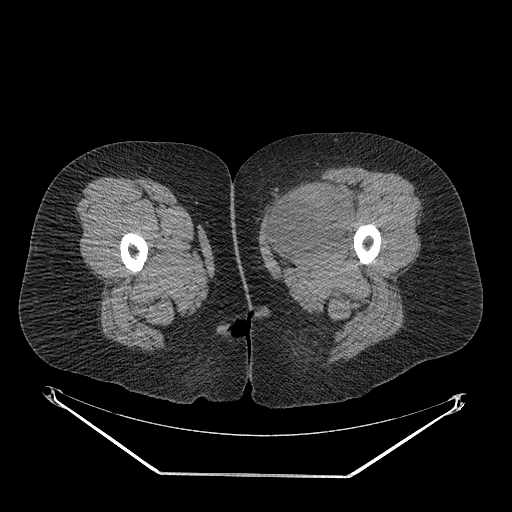
CT of an extremity soft-tissue mass (from a PET/CT study), one axial slice. Slice 26 of 267 in the series (ordered by position). Reconstruction kernel STANDARD. Soft-tissue window (W 400 / L 40 HU). 3.75 mm slice thickness. 512 × 512 image matrix, field of view 500 × 500 mm. Female patient. Case-level facts recorded for this patient, not image findings: histological type: myxofibrosarcoma; grade: intermediate; site of the primary tumour: left thigh.
Annotated regions visible in this slice (expert contour drawn on MRI and transferred to this co-registered scan by the dataset authors):
- gross tumour volume including surrounding oedema: bounding box (x1, y1, x2, y2) in pixels: (265, 185, 357, 257)
- gross tumour volume (mass): (267, 190, 353, 255)